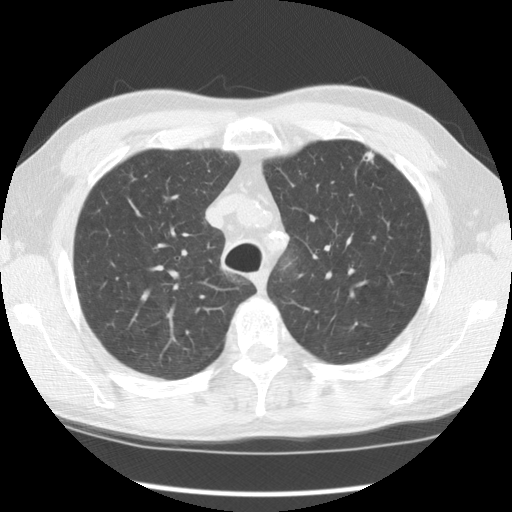
Low-dose screening chest CT, axial slice, baseline screening round, lung window (W 1500 / L -600 HU), standard (soft-tissue) reconstruction kernel (STANDARD), 512 × 512 image matrix, field of view 350 × 350 mm. Male participant, aged 55 years at enrolment. Current smoker at enrolment.
Lesion marked by an expert reader, bounding box <350,138,392,180> (left, top, right, bottom; pixels). The exam's reader record, not a measurement of the box and not confirmed to be the same lesion: non-calcified nodule or mass ≥4 mm, left upper lobe, 5 × 5 mm, poorly defined margins, soft tissue attenuation. Lung cancer was diagnosed 159 days after this screen: adenocarcinoma, NOS, left upper lobe, moderately differentiated (G2), stage IA (AJCC 6th edition), 8 mm at pathology.